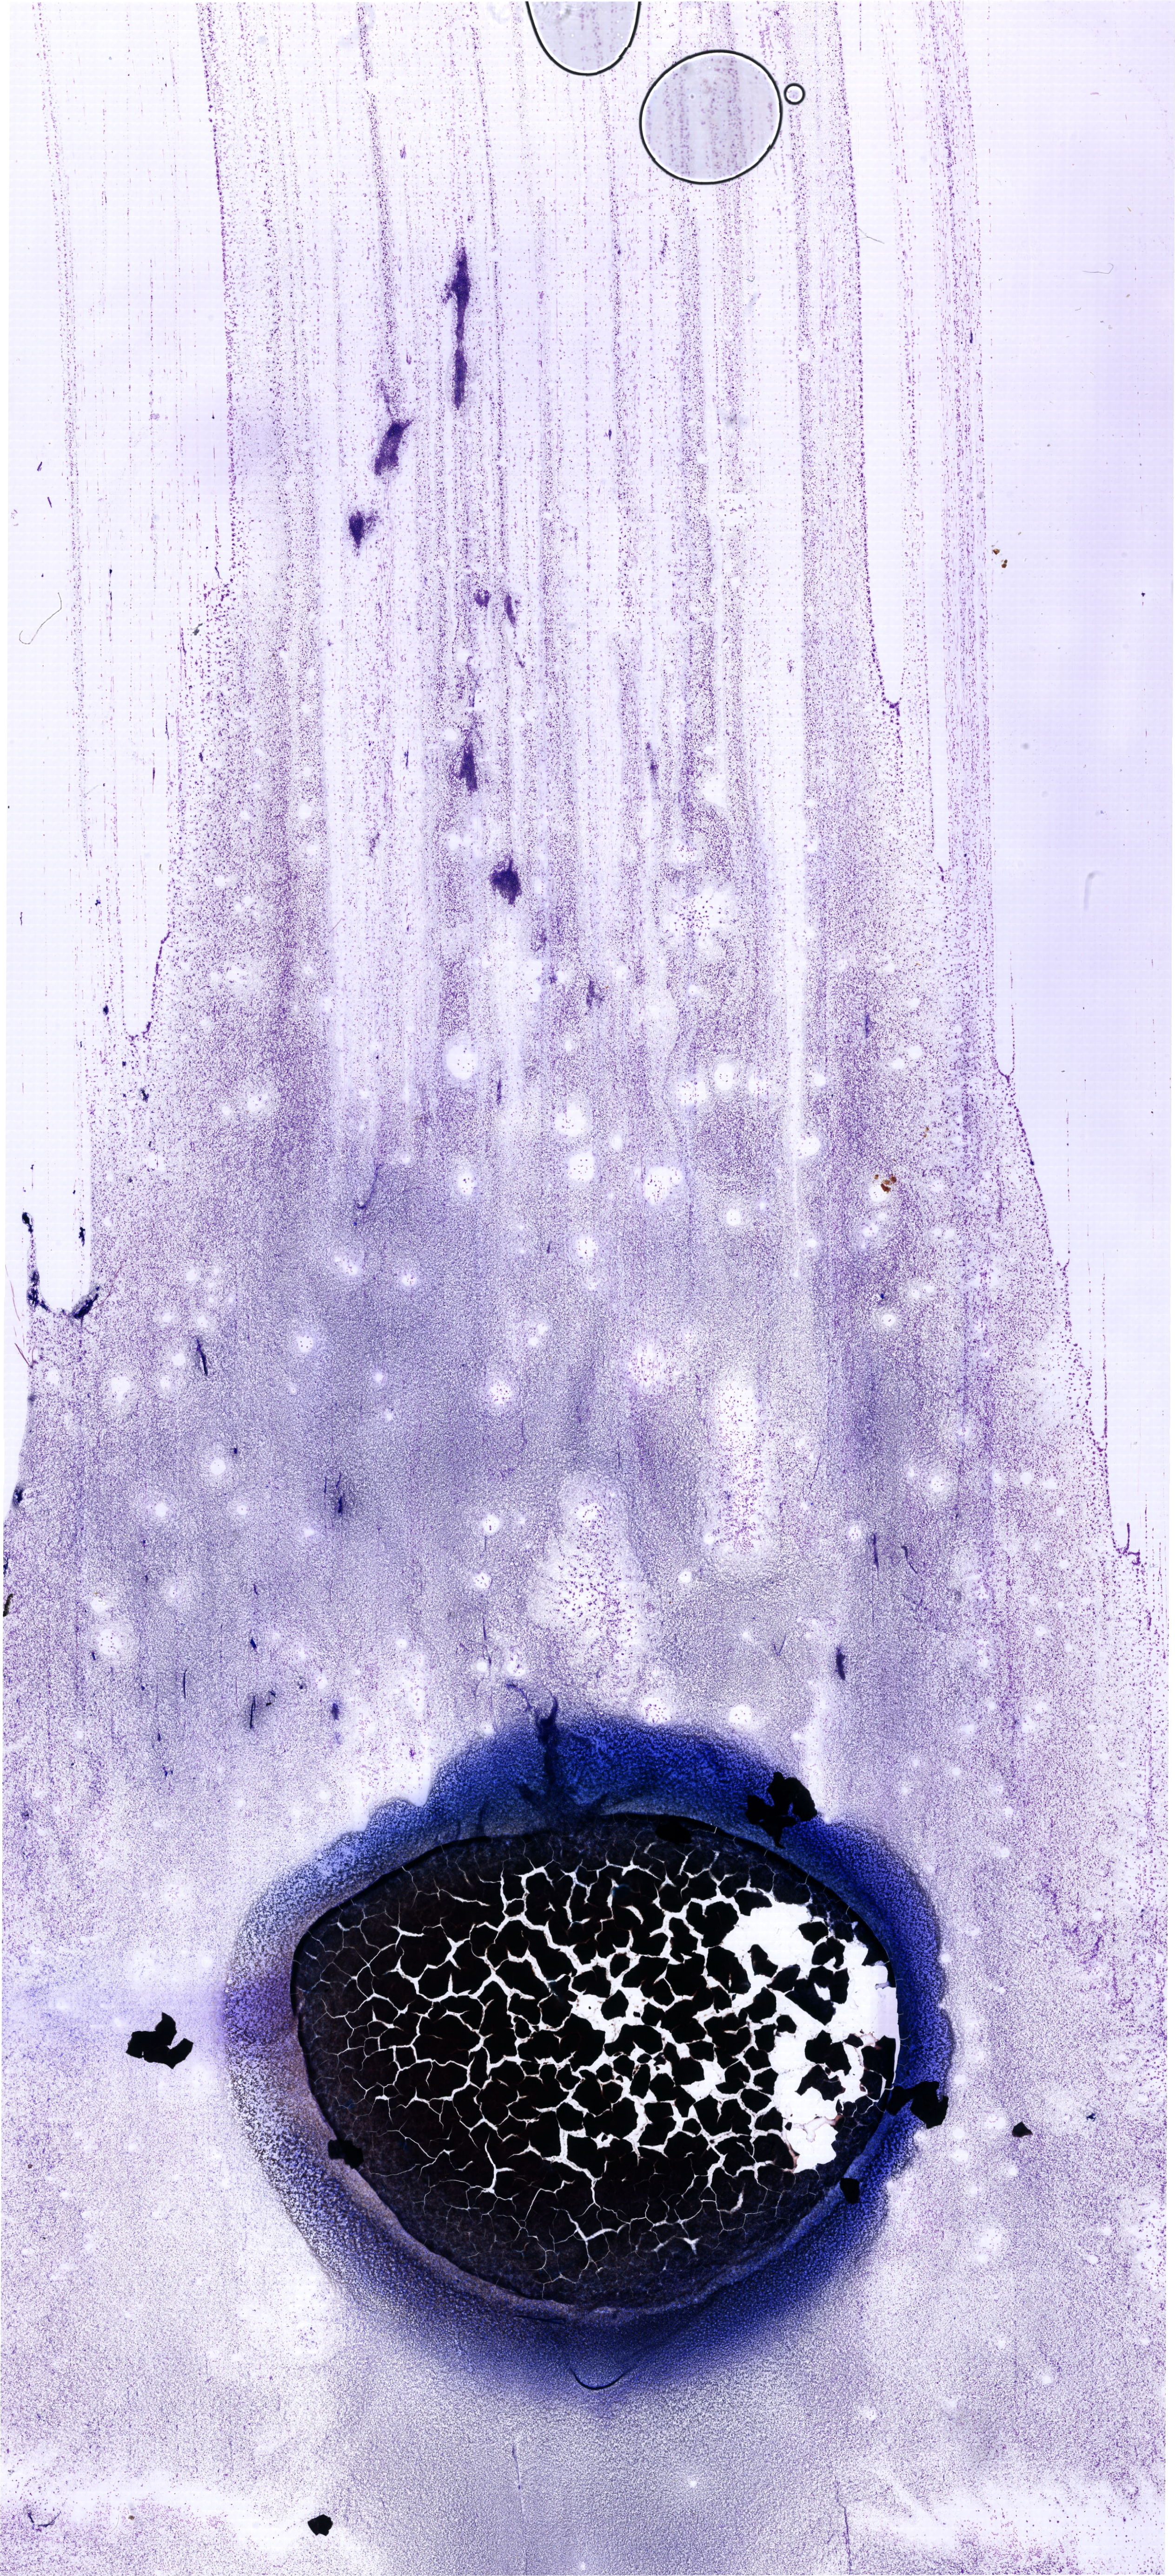
May-Grünwald-Giemsa (MGG)-stained marrow aspirate smear (whole slide), shown as a low-resolution overview of the whole scanned area (about 19.7 x 43.2 mm). Male patient.
Diagnosis: Mixed Phenotype Acute Leukemia, B/Myeloid.